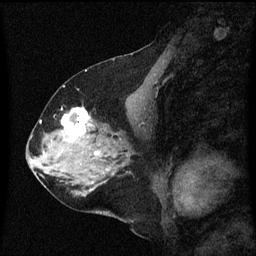
Breast MRI (dynamic contrast-enhanced), one sagittal slice. Slice 28 of 60 in the series (ordered by position). Dynamic contrast-enhanced series, image 2 of 3 at this slice position (ordered by acquisition). 1.5 T. TE 4.2 ms, TR 8 ms. 256 × 256 image matrix, field of view 200 × 200 mm. Female patient, age 58 years.
Annotated regions visible in this slice (semi-automatically segmented with operator editing):
- analysis volume of interest (the breast-tissue region the enhancement analysis was run in; not a lesion): bounding box [x1, y1, x2, y2] px = [56, 108, 99, 149]
- tumour enhancement mask (voxels above the 70 % enhancement threshold inside the analysis volume of interest): [63, 108, 91, 141]